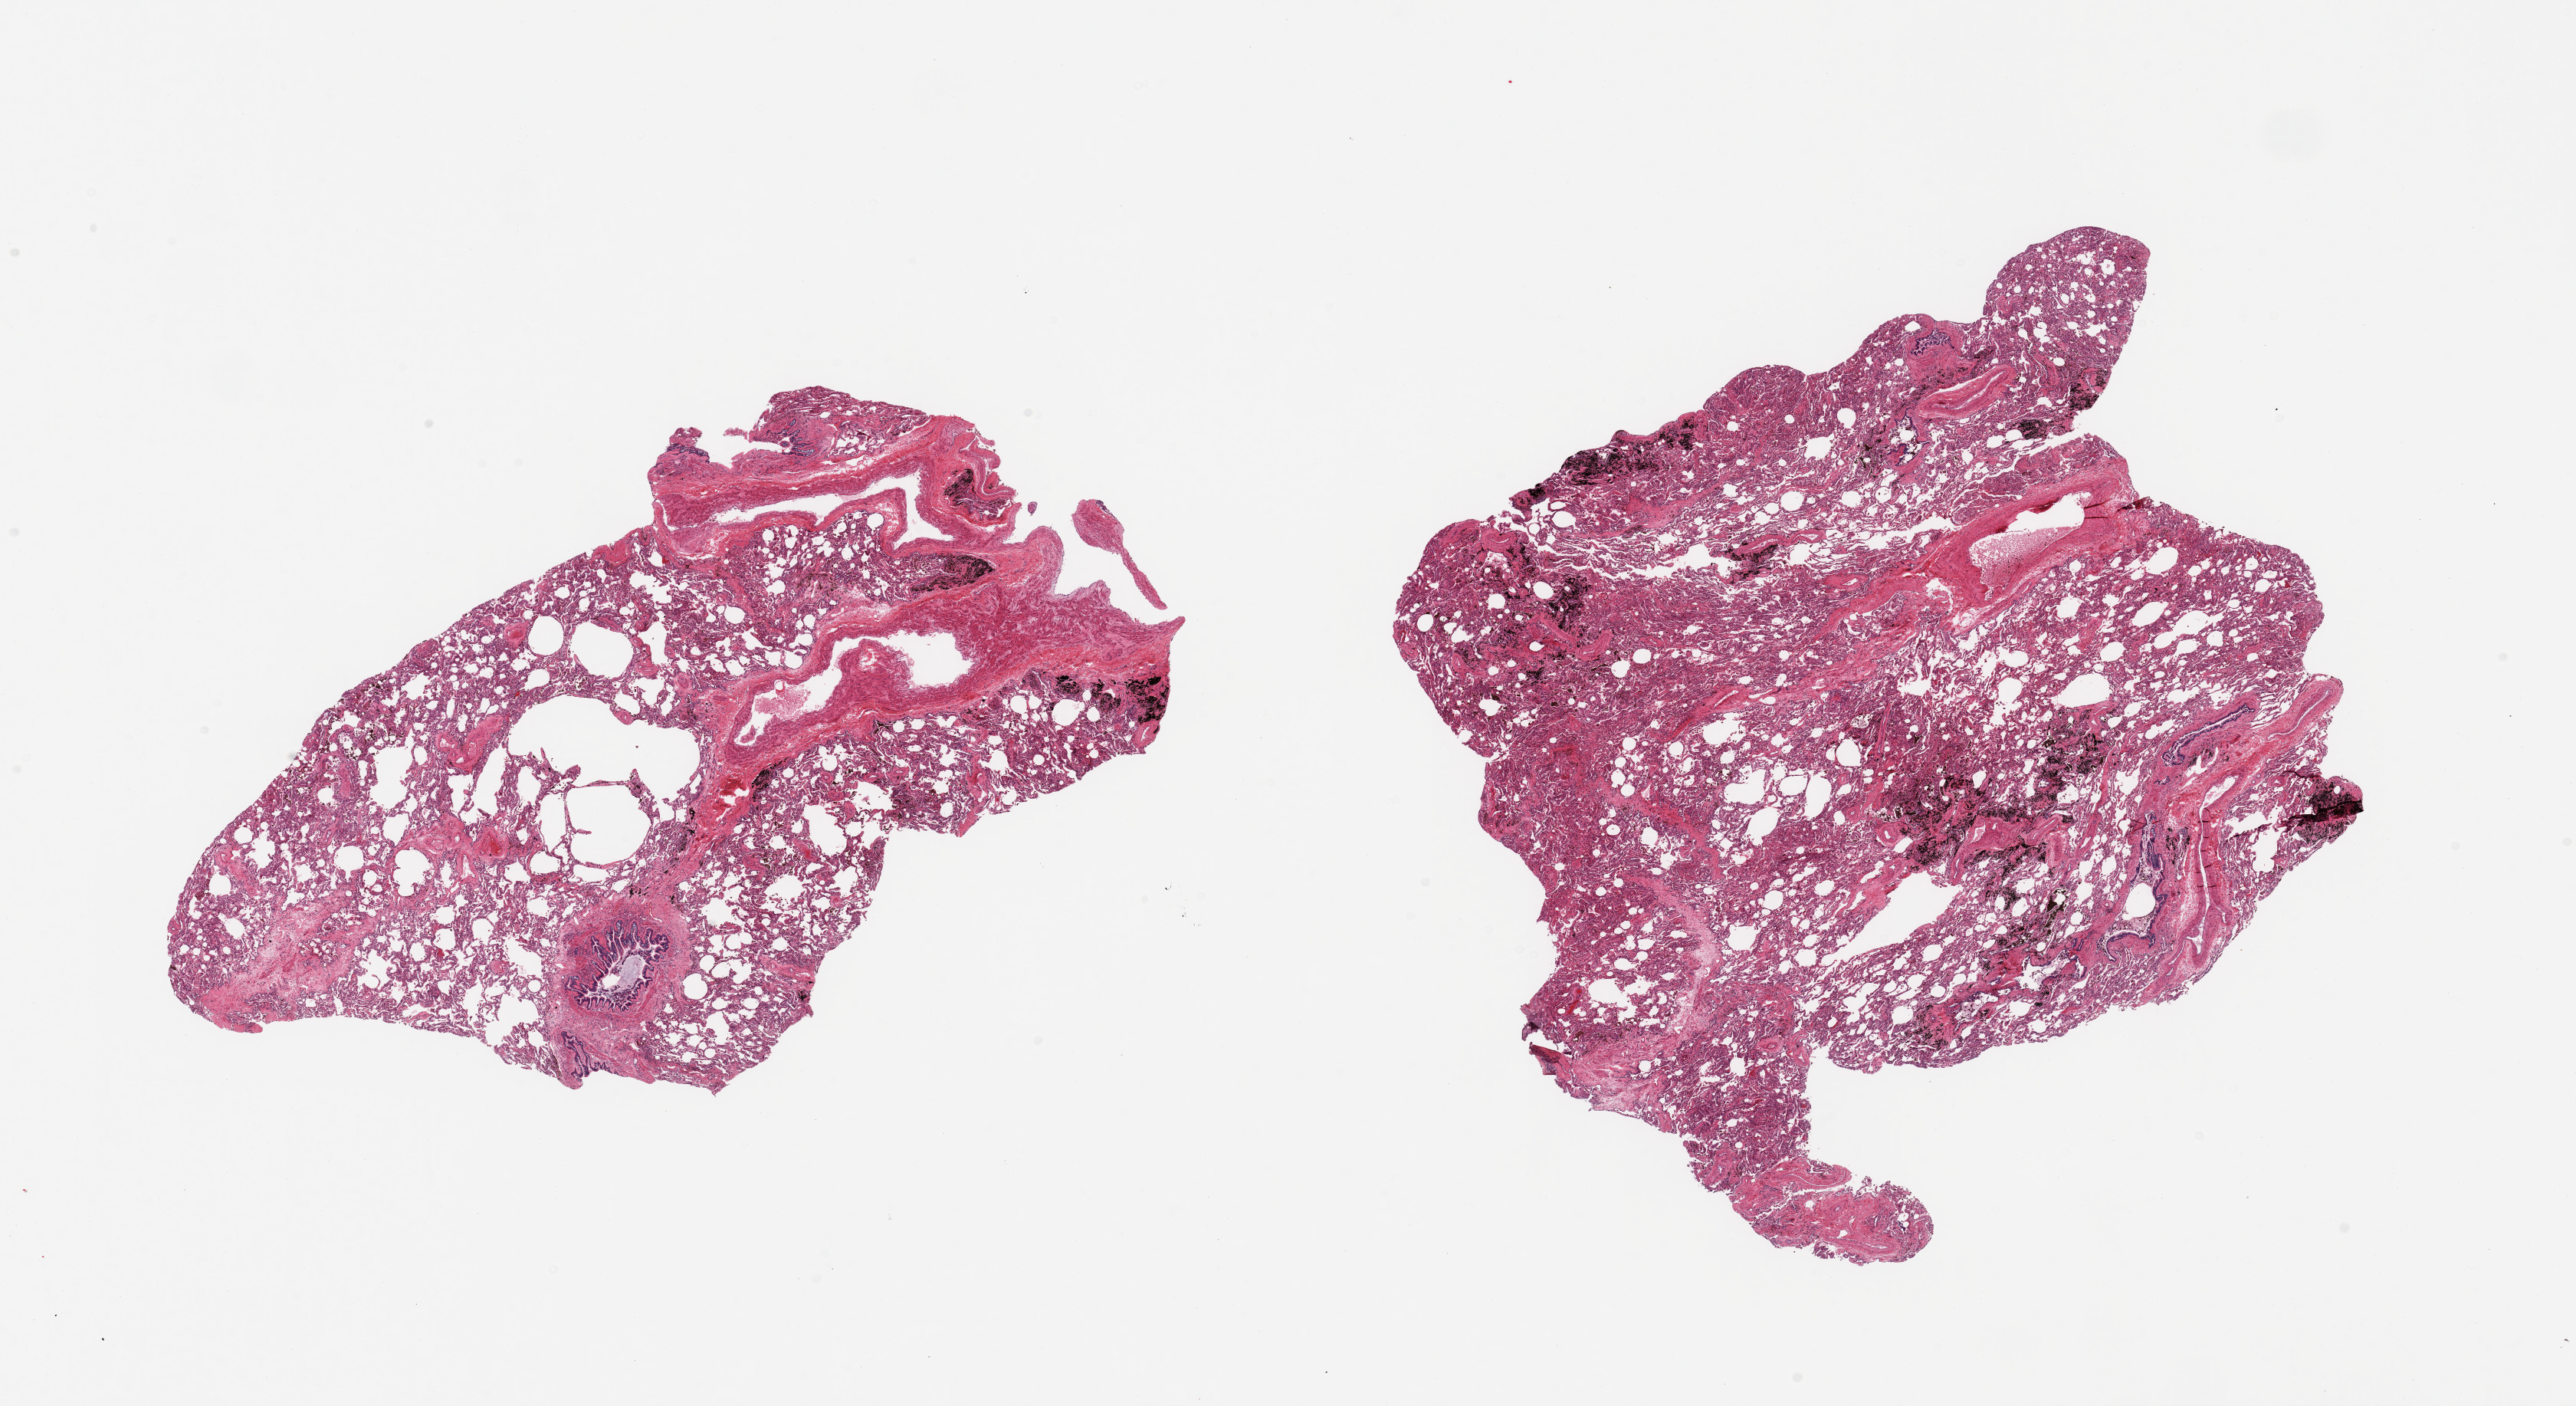
Digitized hematoxylin and eosin (H&E)-stained section — shown as a low-resolution overview of the whole scanned area (about 26.6 x 14.5 mm, acquisition: 20x scan), PAXgene-fixed paraffin-embedded (PFPE) section, section of lung (target tissue), tissue donor sample.
Pathologist's review note for this sample: 2 pieces; emphysema, fibrosis, vascular sclerosis, focal anthracotic pigment, pigmented alveolar macrophages; large vessels and bronchus comprise 20% of 1 piece.